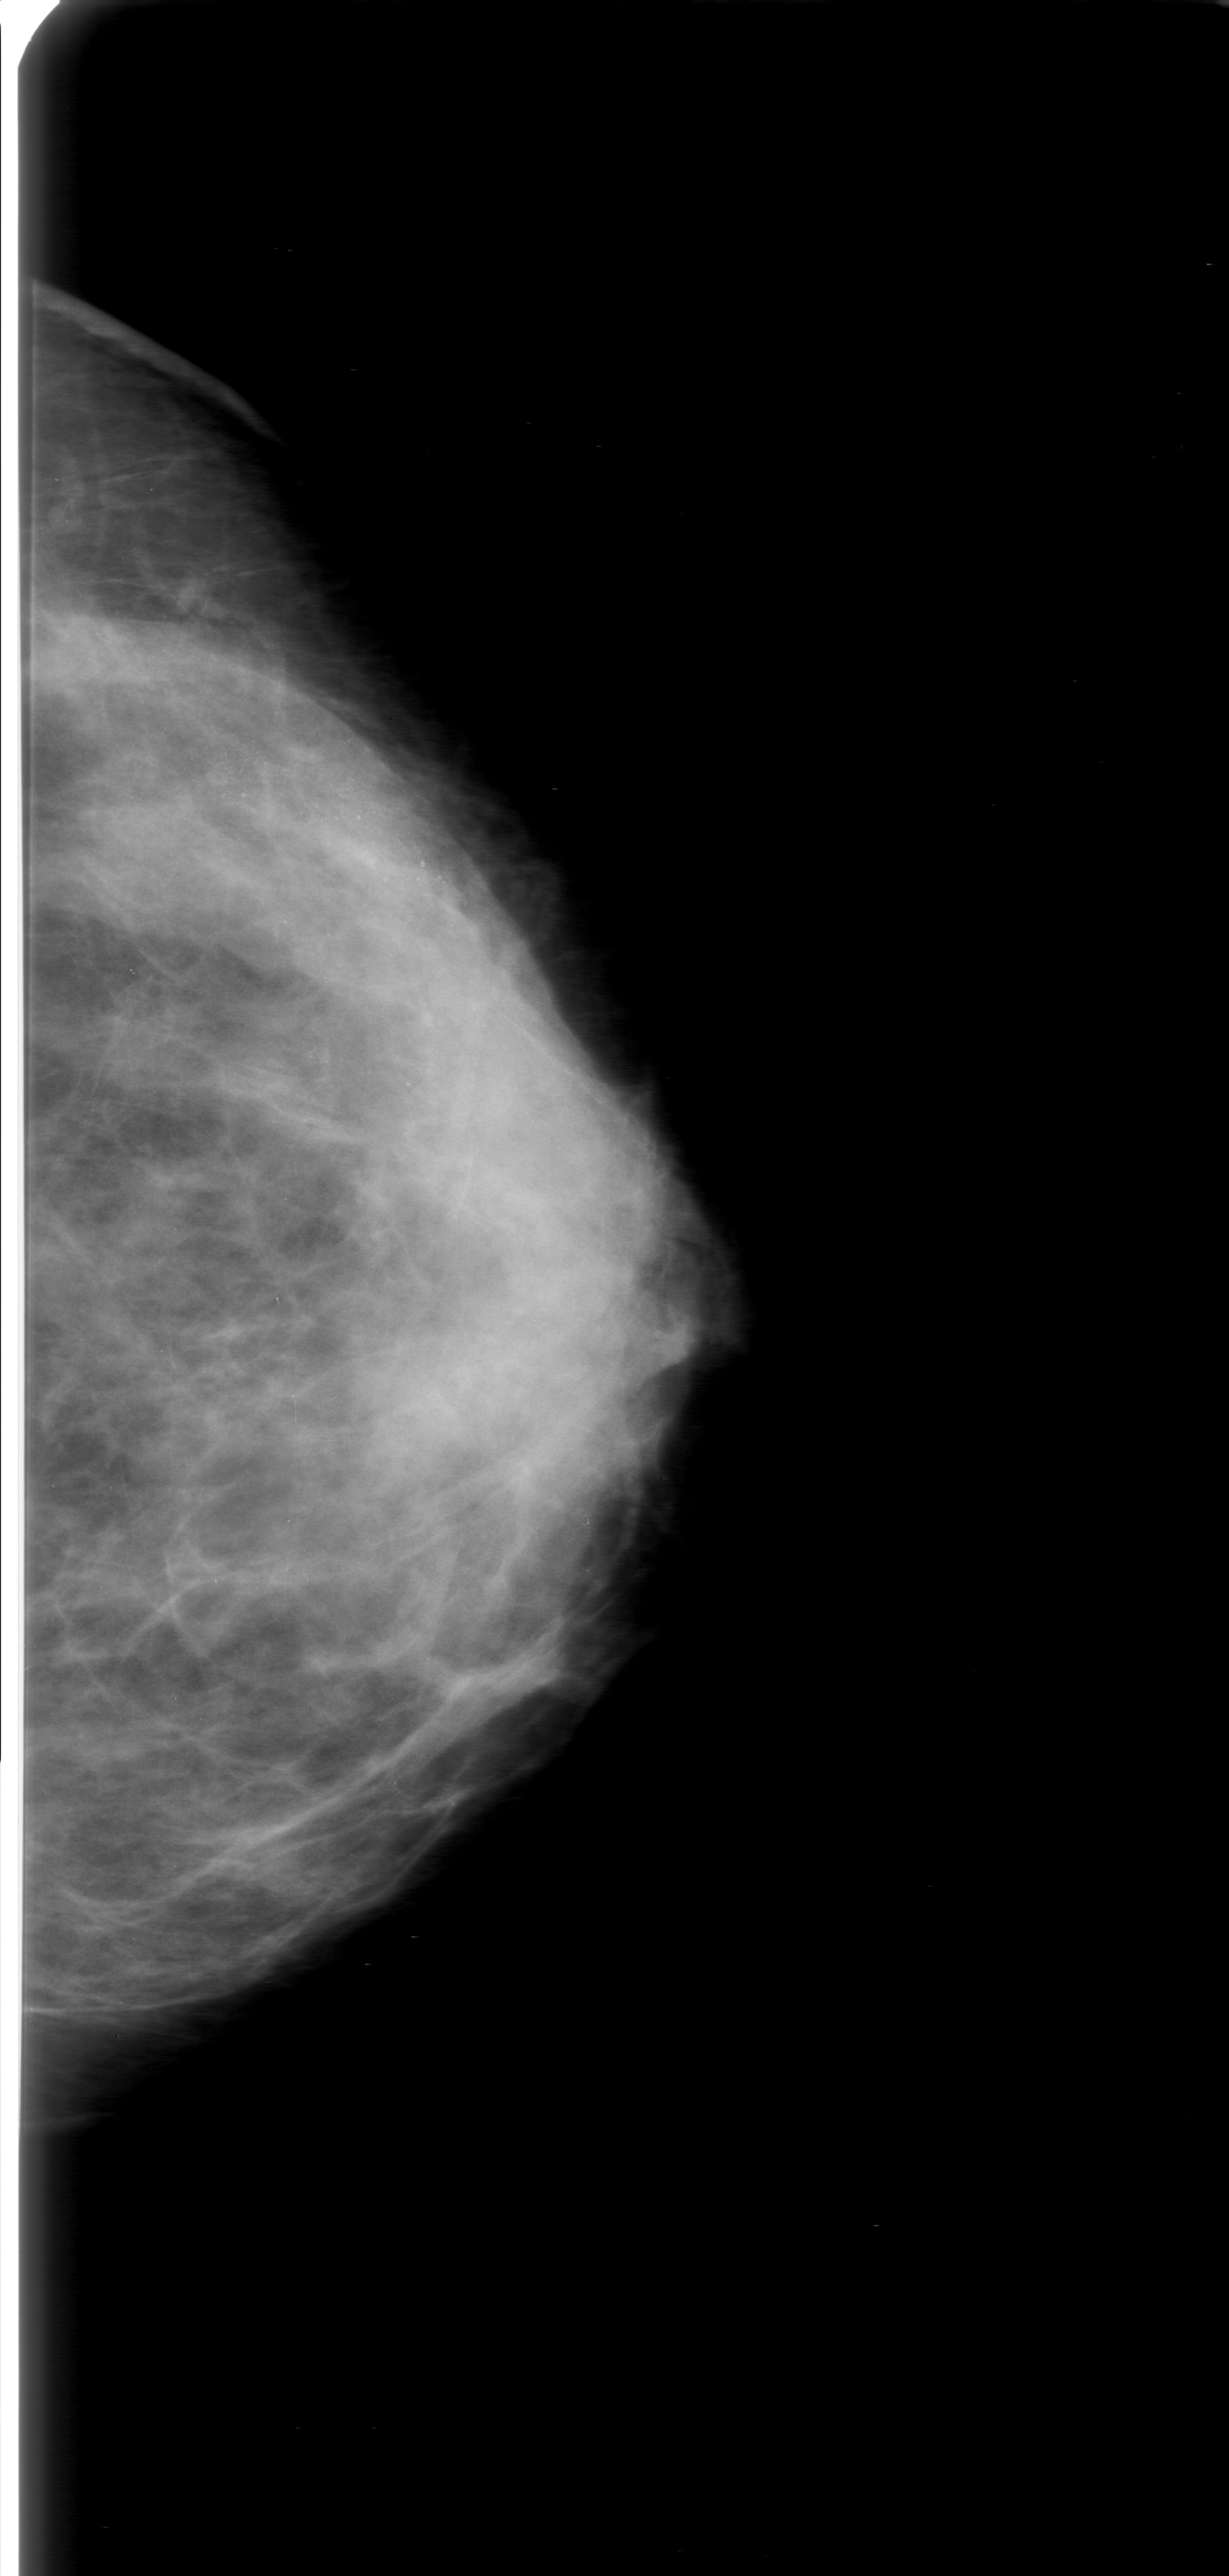
Scanned film-screen mammogram. Left breast. CC view. BI-RADS breast density category 3 (scale 1–4). 1229 × 2576 image matrix.
Marked abnormalities (boxes around the expert regions of interest):
- calcifications, morphology amorphous, distribution segmental; BI-RADS assessment category 0 (incomplete: needs additional imaging); pathology result (as recorded, not read from the image): benign: bounding box [x1, y1, x2, y2] px = [117, 558, 592, 1116]